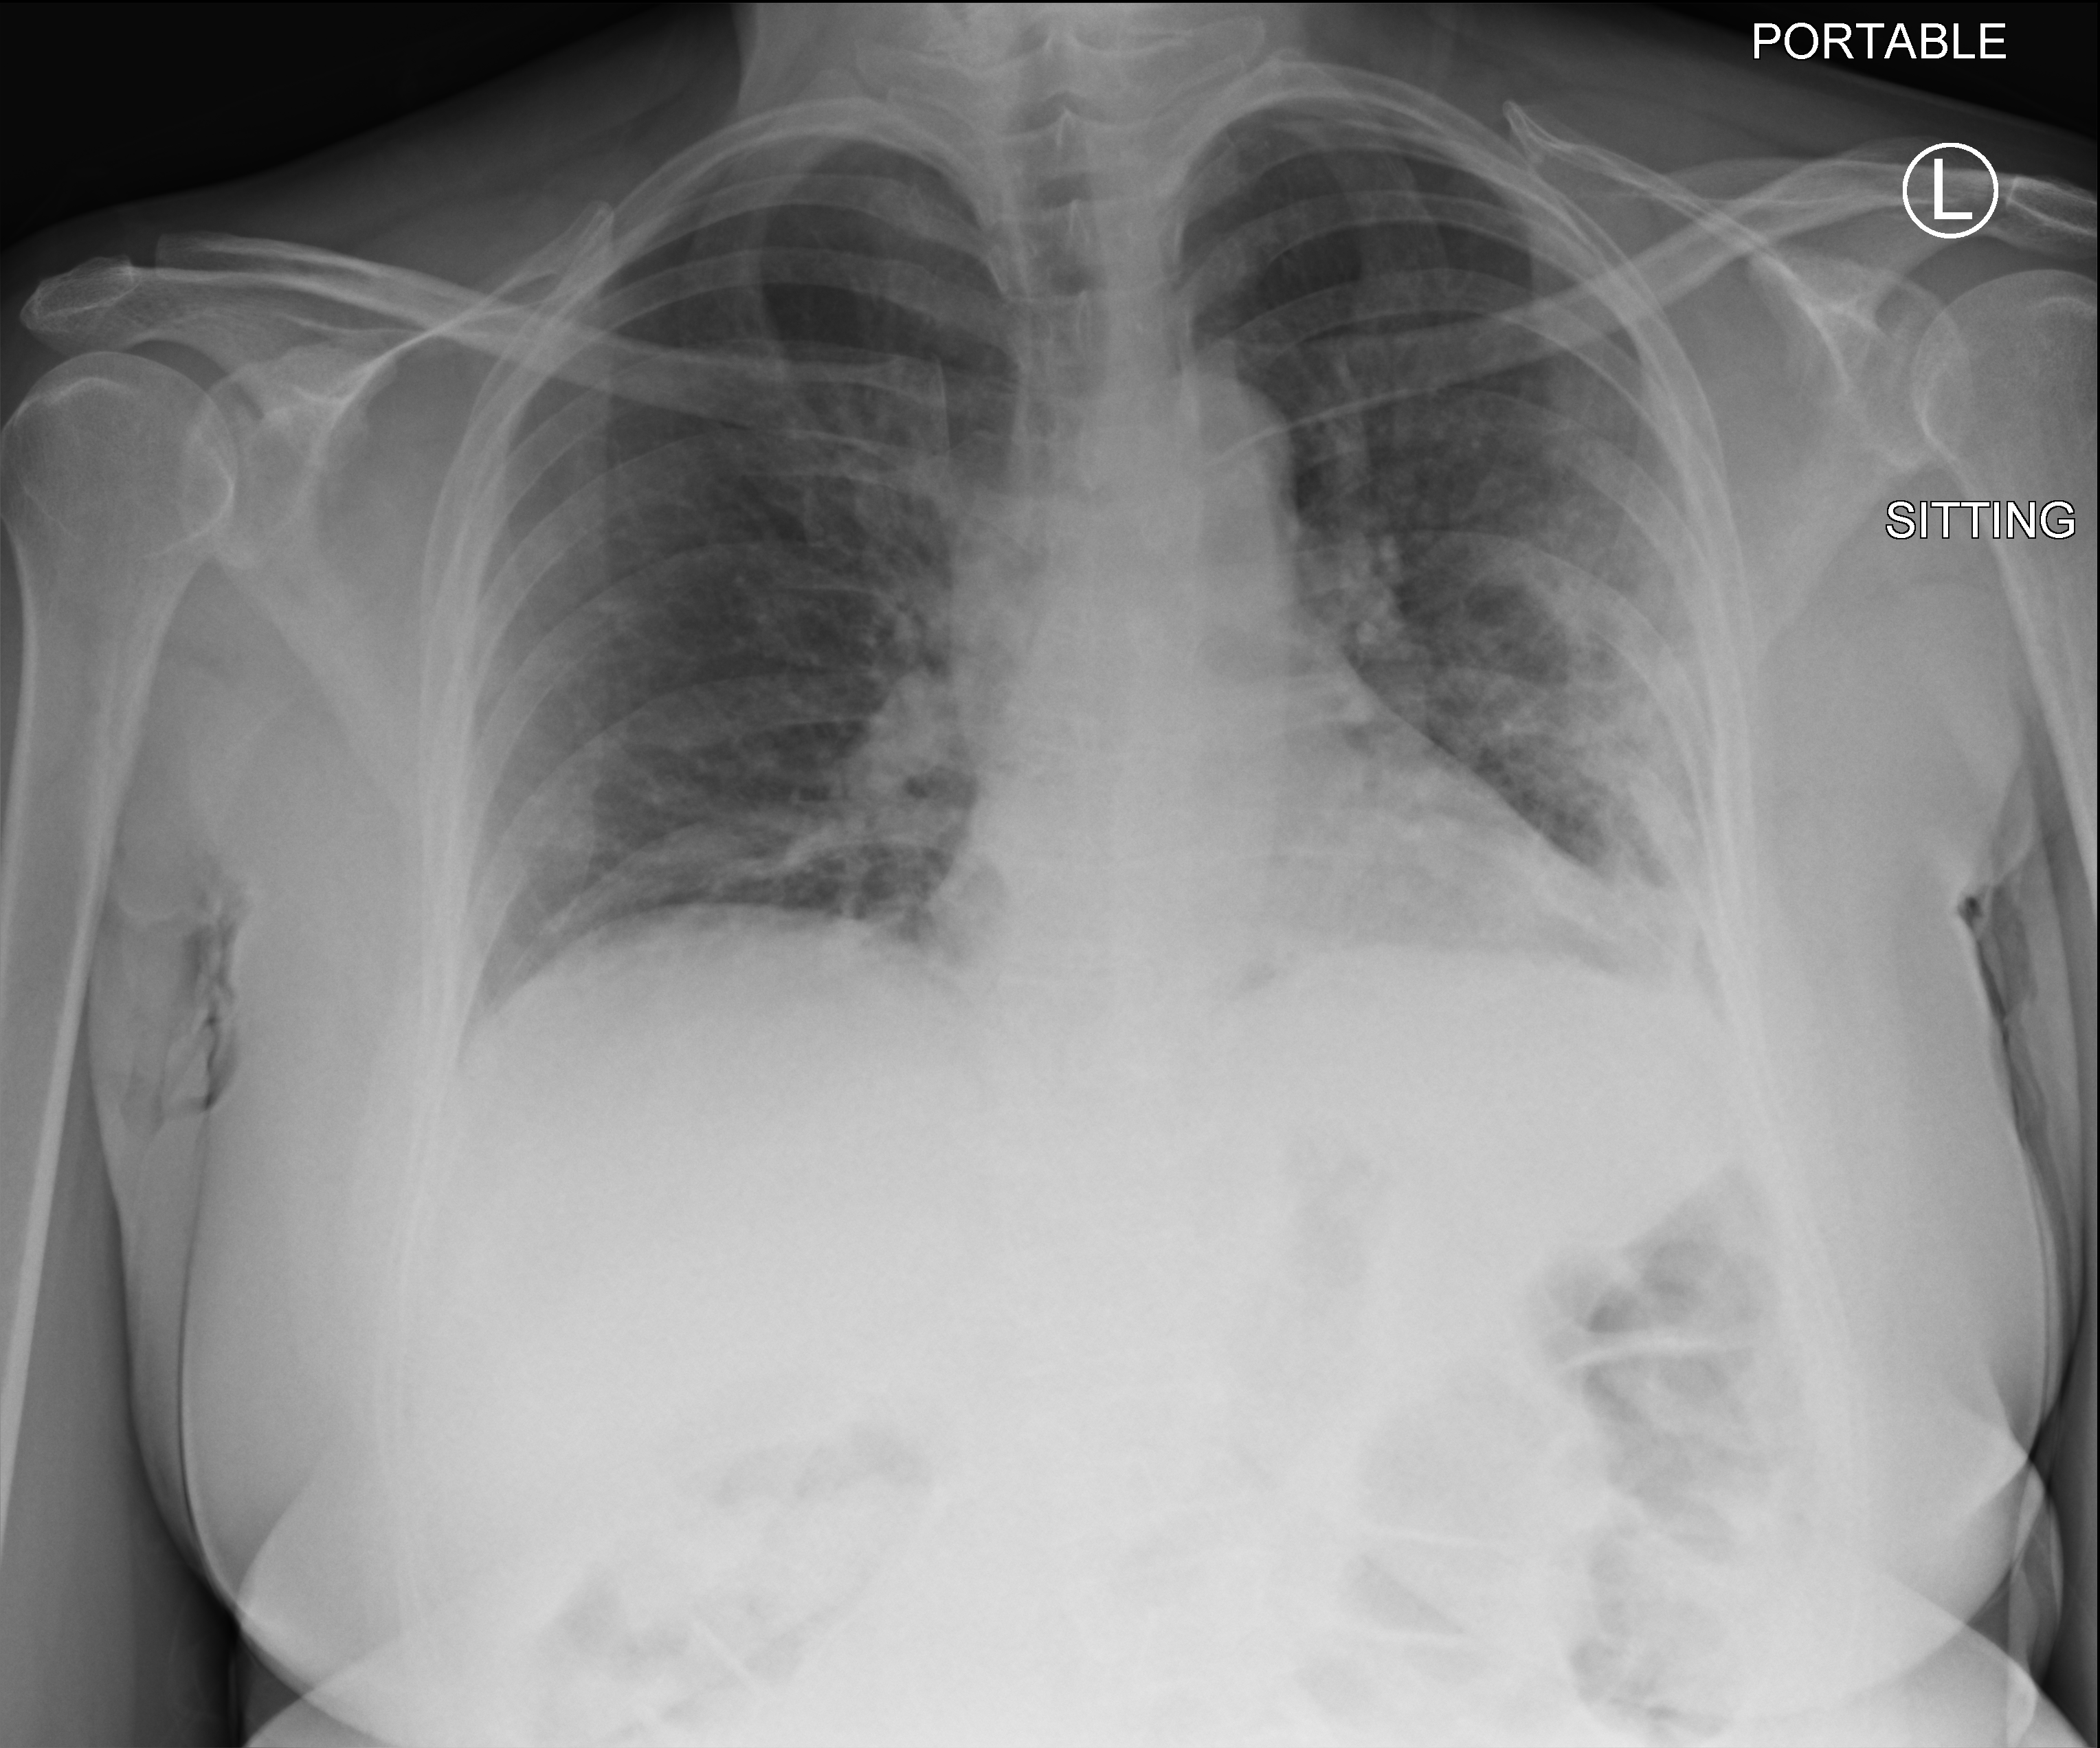
Portable chest radiograph, anteroposterior (AP) projection. Patient hospitalised with COVID-19; female, aged 18–59 years.
Hospital-stay facts (about this admission, not read from this image; timing relative to this image not recorded):
- length of hospital stay: 3 days